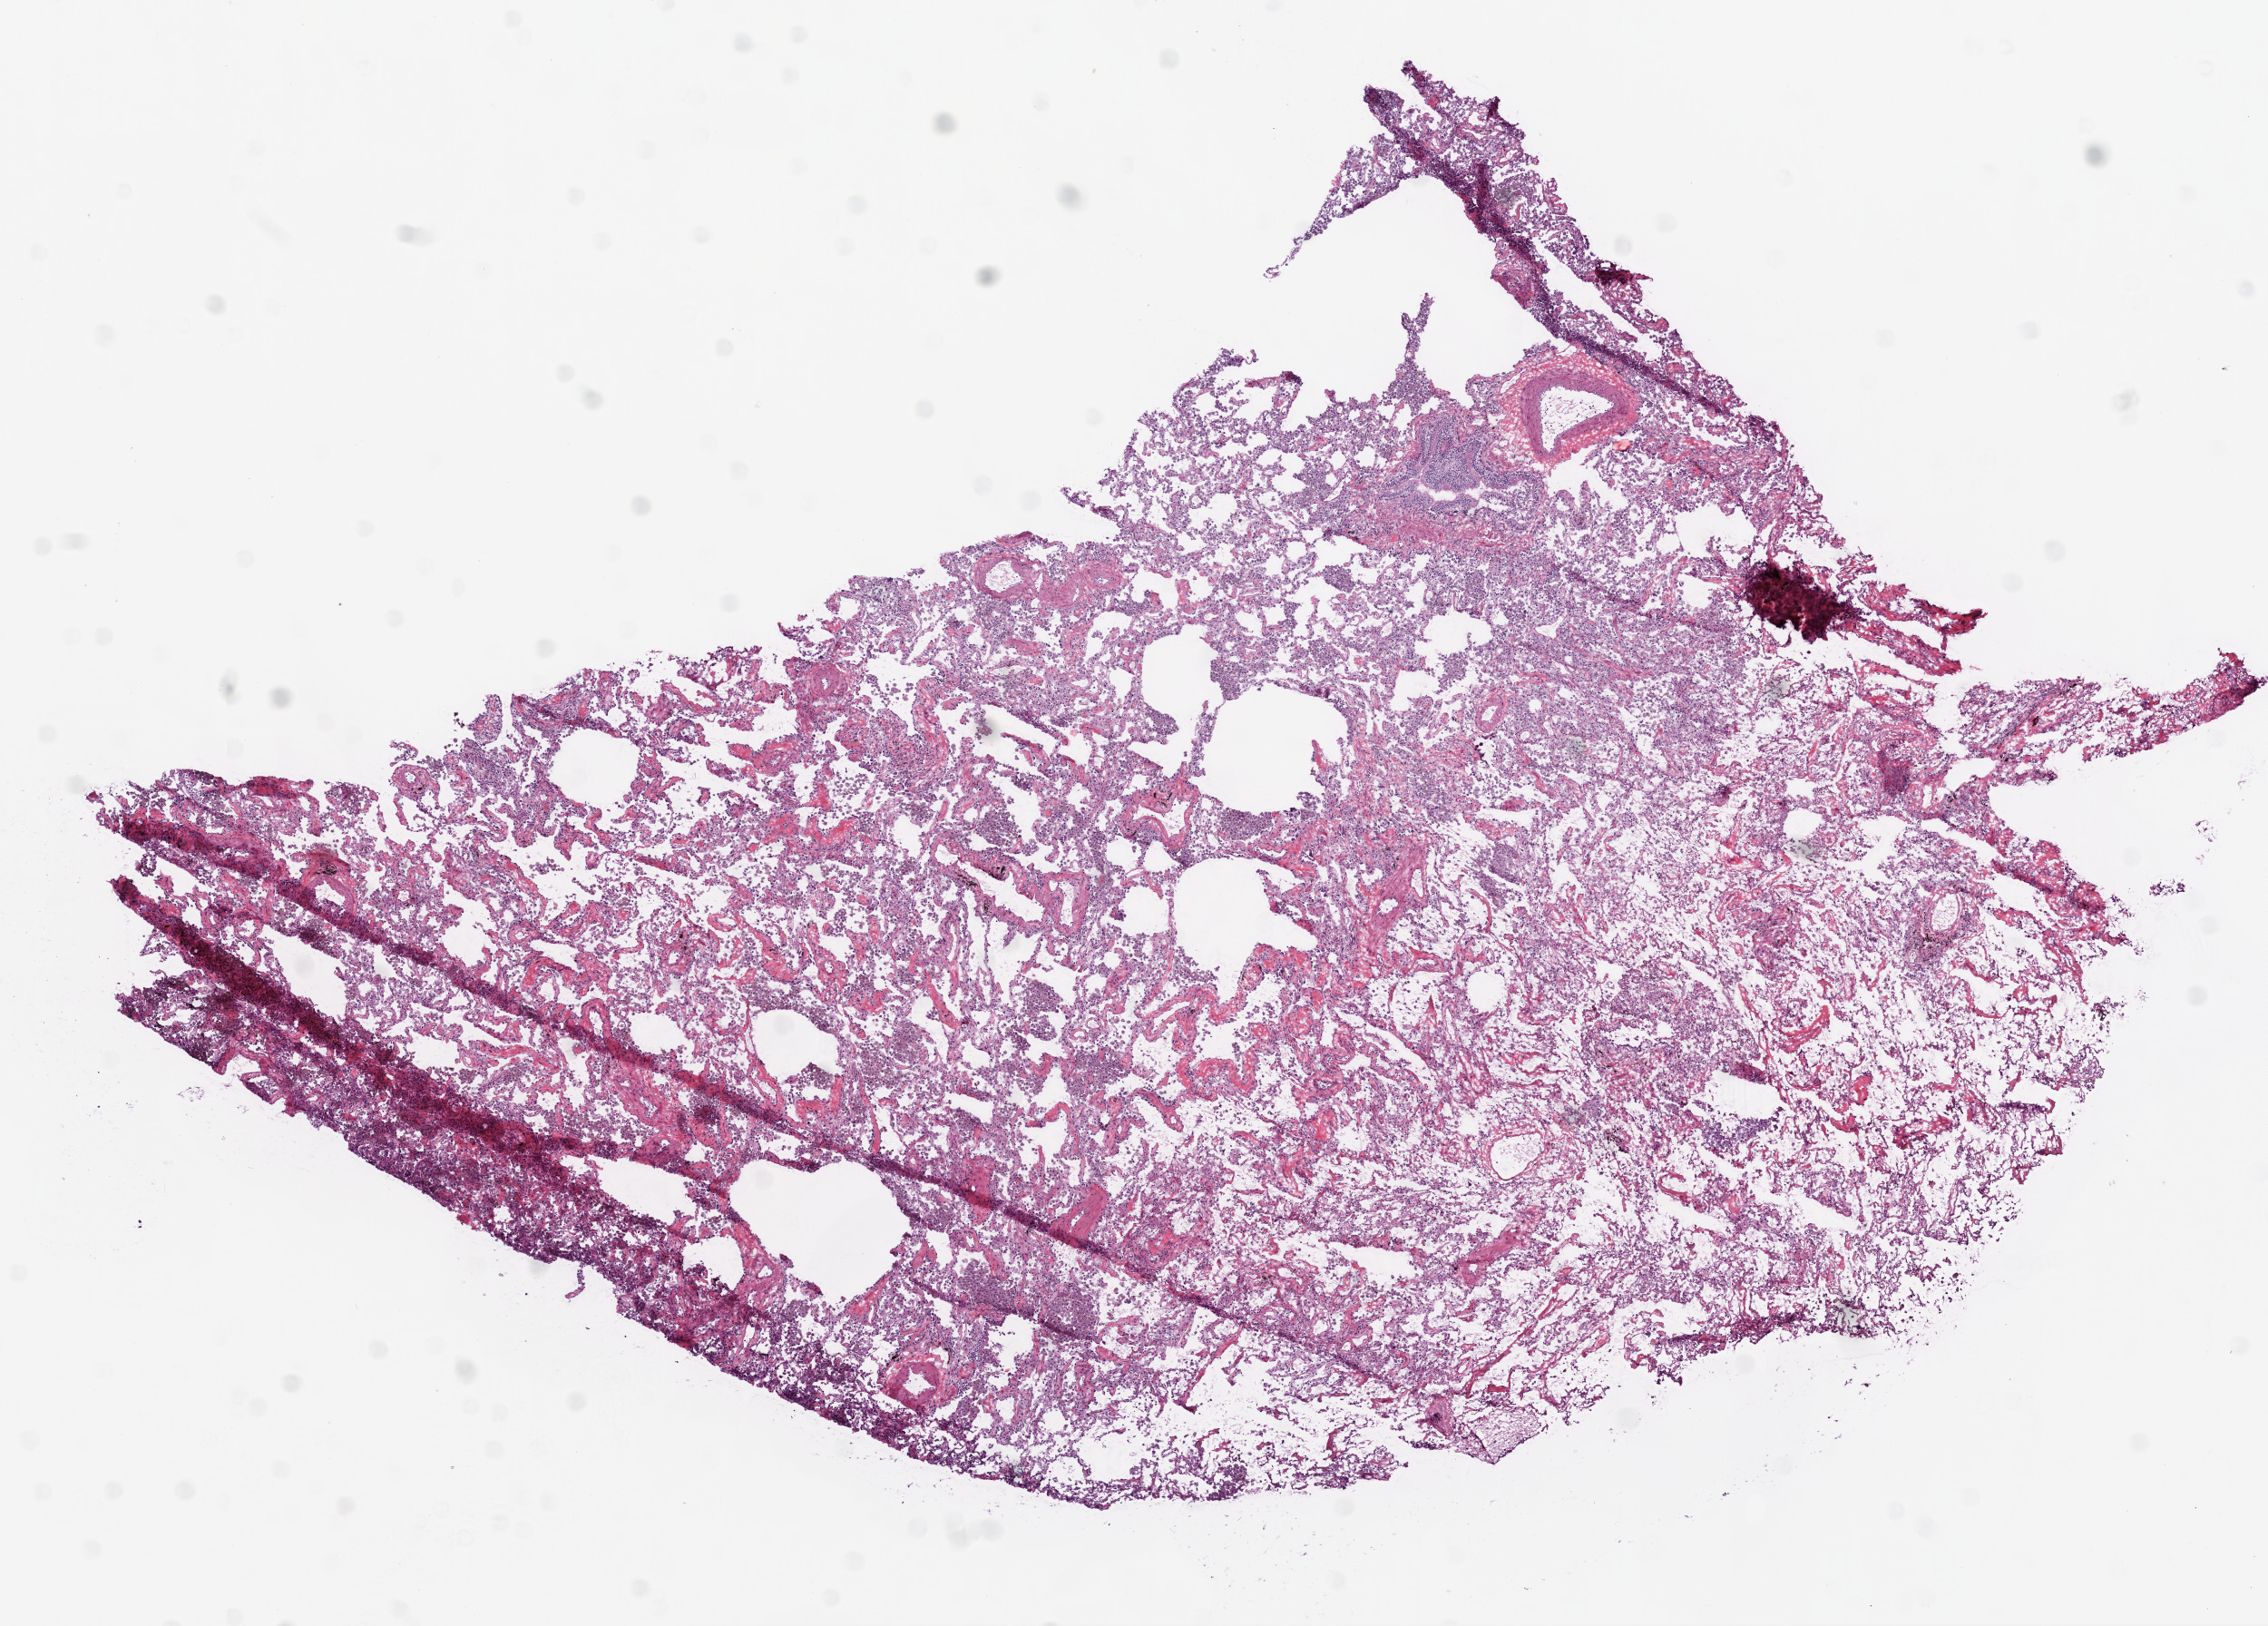
Digitized H&E tissue section (whole slide) — whole scanned area (about 10.0 x 7.2 mm) shown as a low-resolution overview; frozen section; solid tissue normal (non-tumour tissue) sample from the lung. Male patient; age at initial diagnosis 64 years.
This section: solid tissue normal sample (biorepository sample class). Patient diagnosis: Squamous cell carcinoma, NOS (lower lobe, lung).